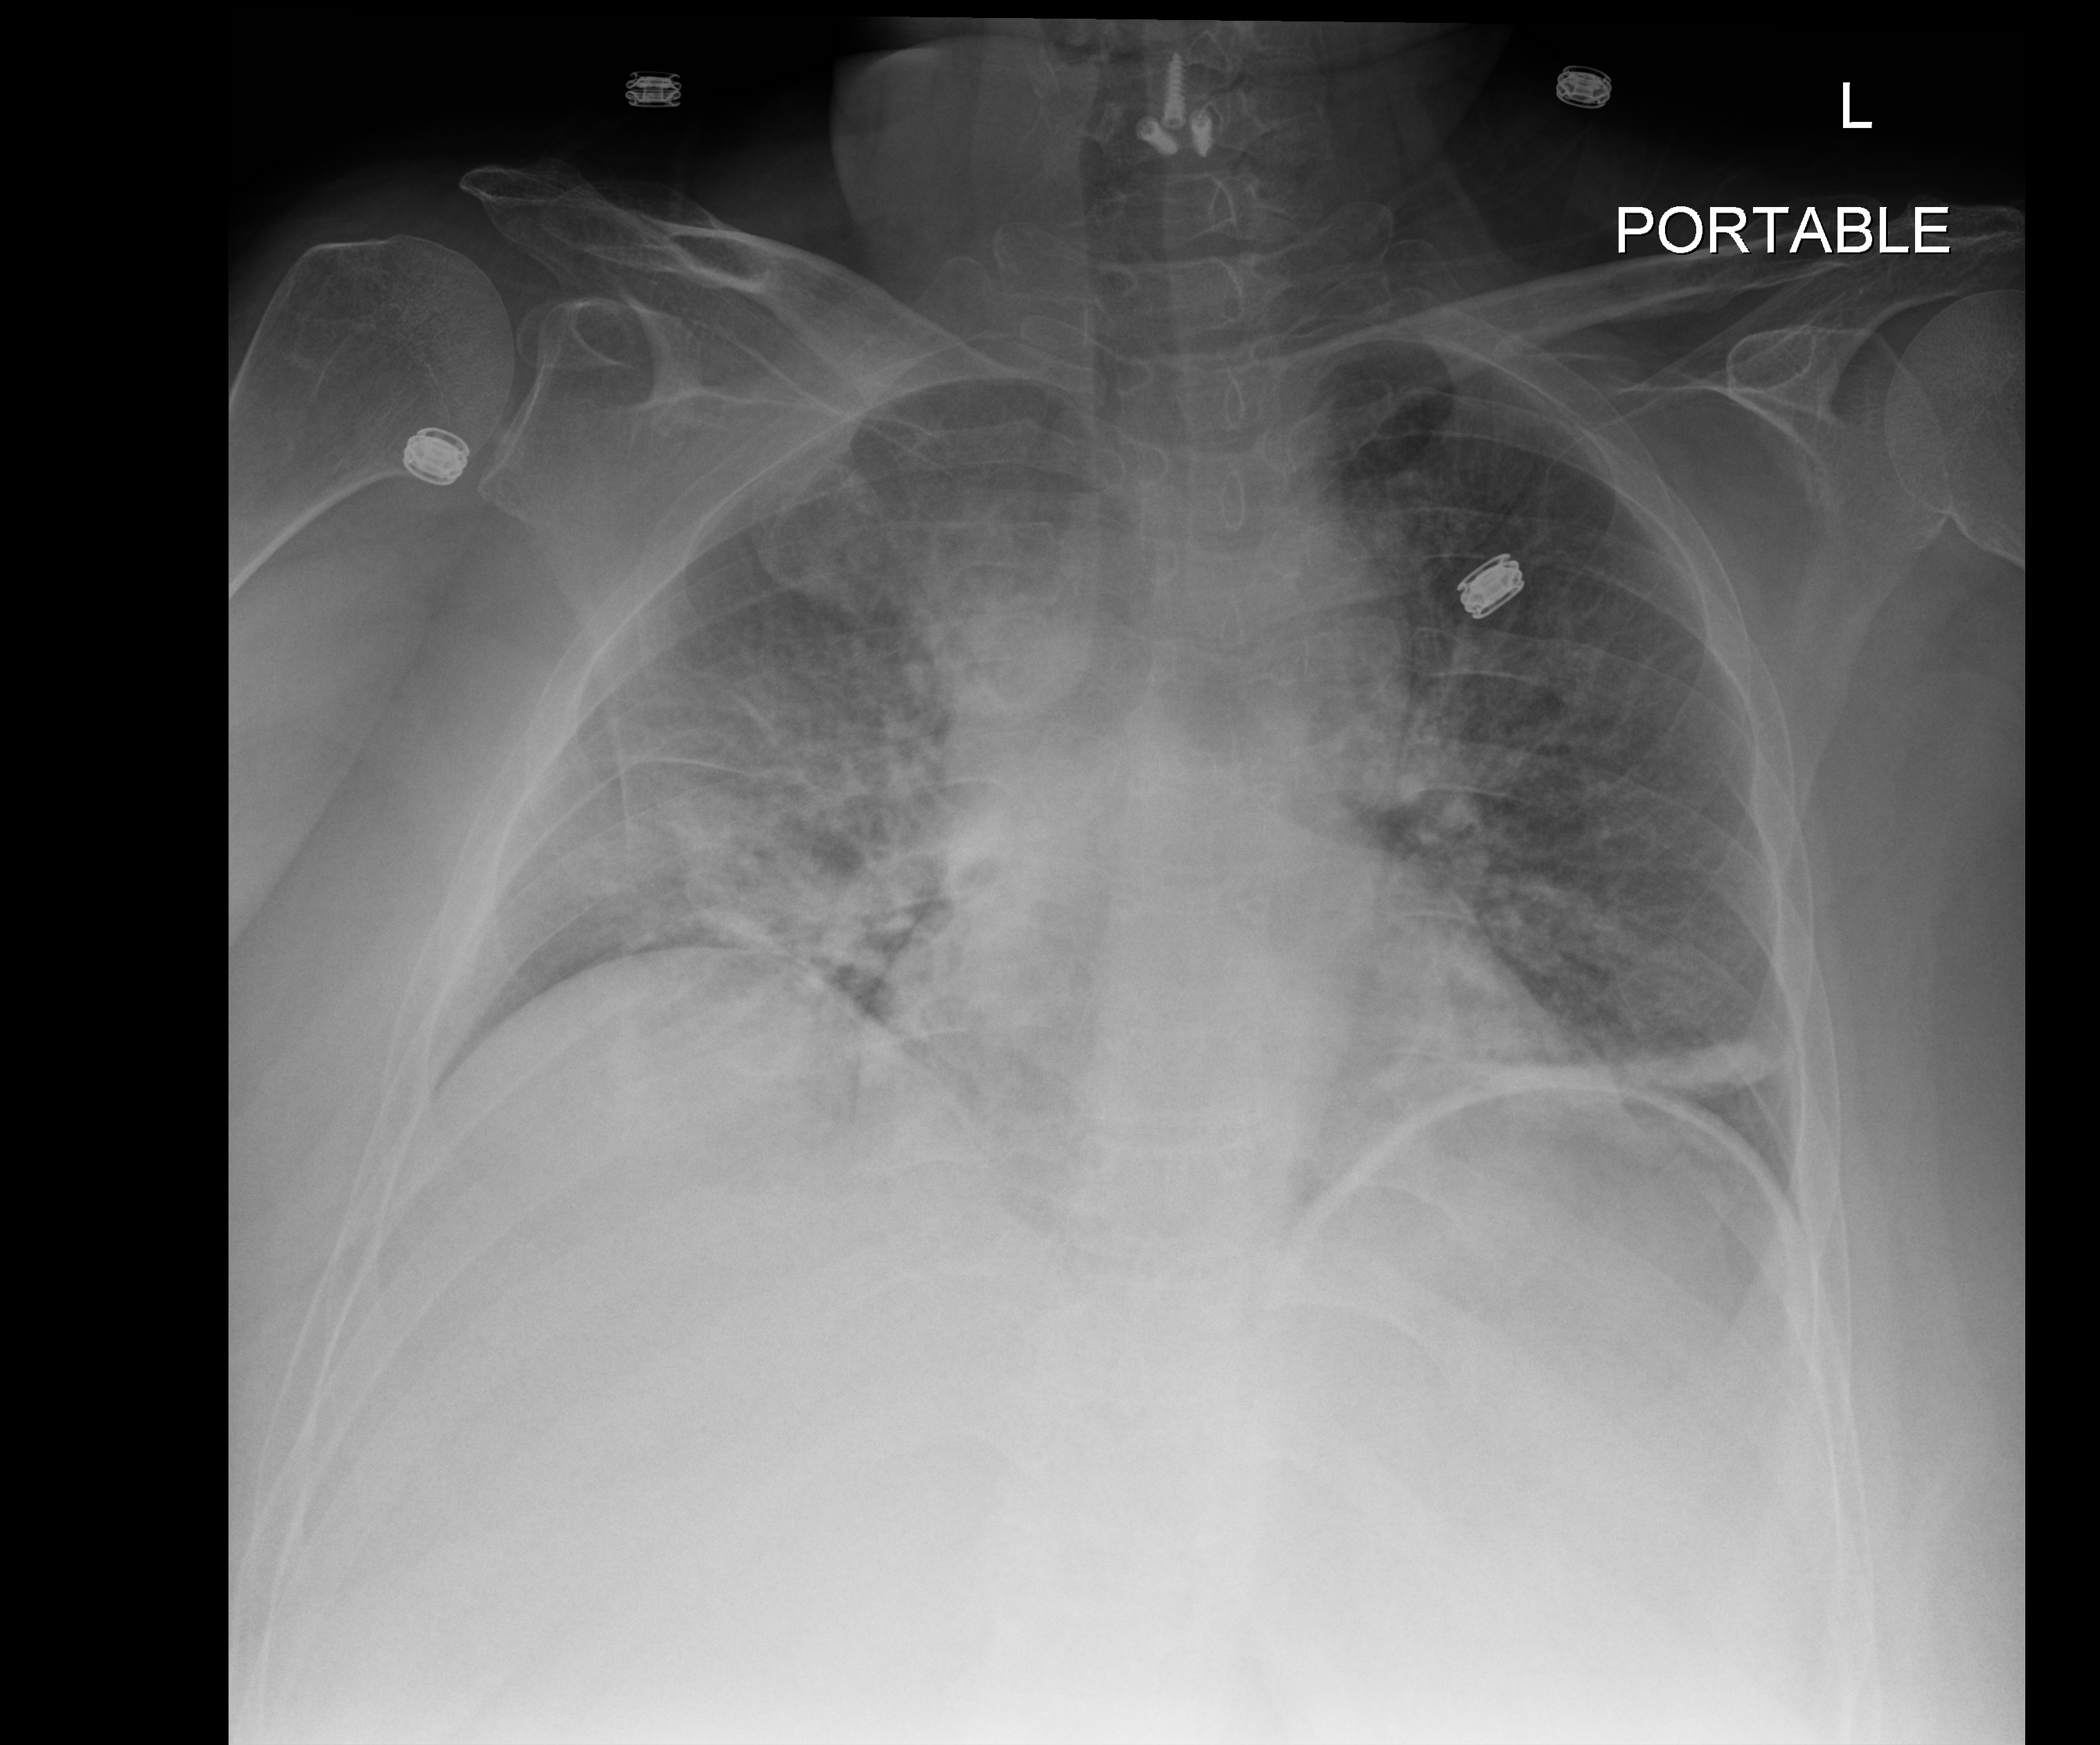
Chest radiograph (digital radiography); anteroposterior (AP) projection. Female patient hospitalised with COVID-19, age 18–59 years.
Hospital-stay facts (about this admission, not read from this image; timing relative to this image not recorded):
- mechanically ventilated during this hospital stay: no